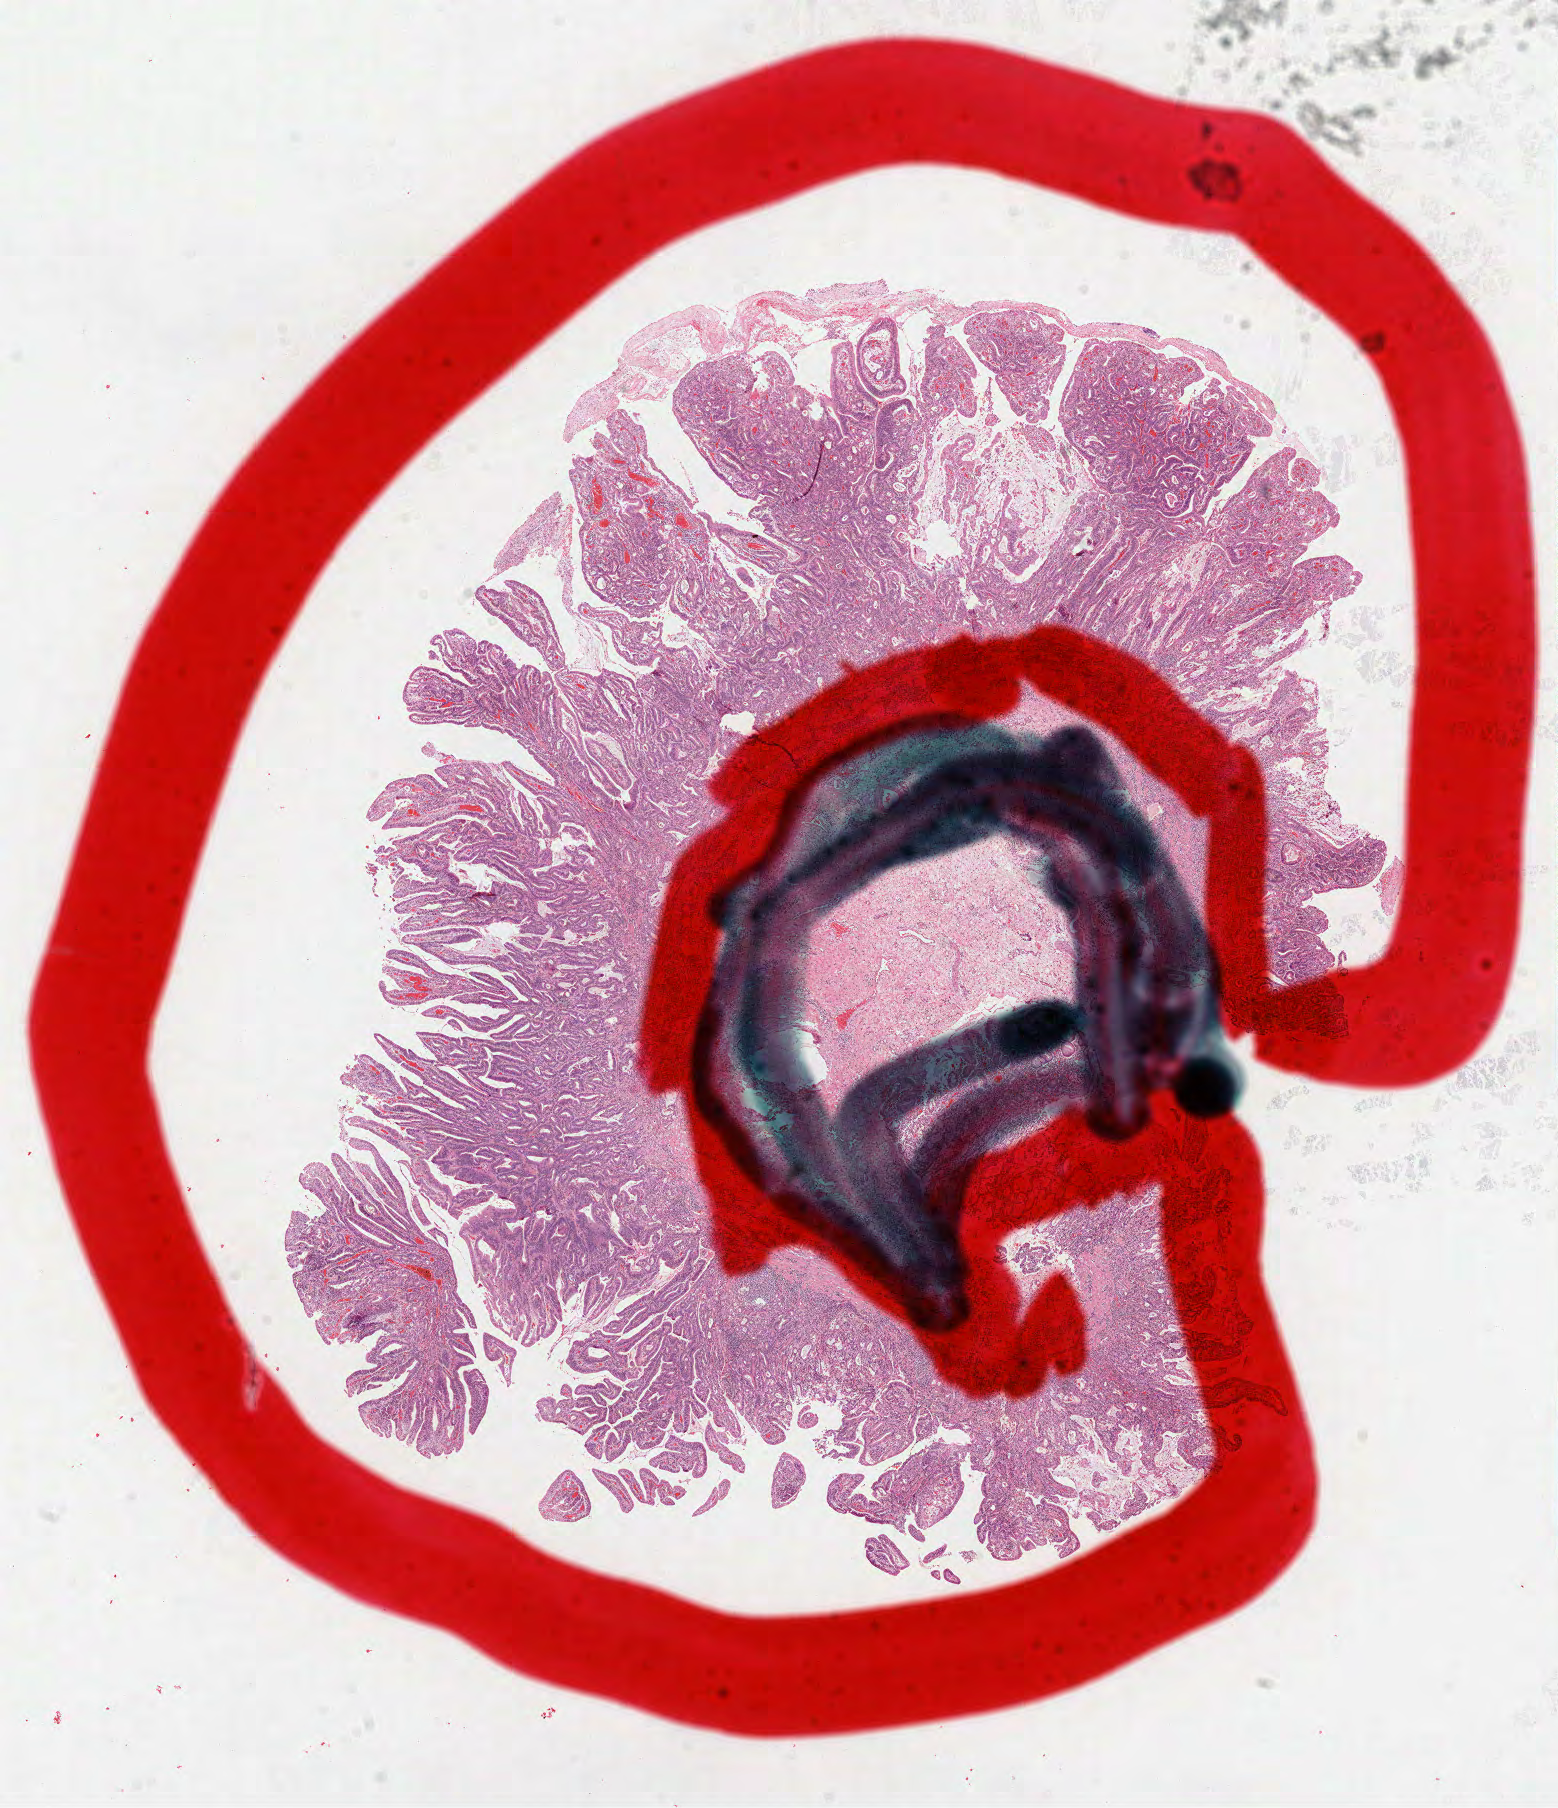
Whole-slide histology image, H&E-stained — low-resolution overview of the scanned area, about 12.6 x 14.6 mm (slide scanned at 40x), FFPE section, primary tumour sample from the stomach. Male, age 81 years at initial diagnosis. Histologic grade: G2 (moderately differentiated).
- TNM: T1b N0 M0
- diagnosis: Papillary adenocarcinoma, NOS (body of stomach)
- lymph nodes positive (case pathology): 0 of 4 examined
- AJCC pathologic stage: IA (7th edition)